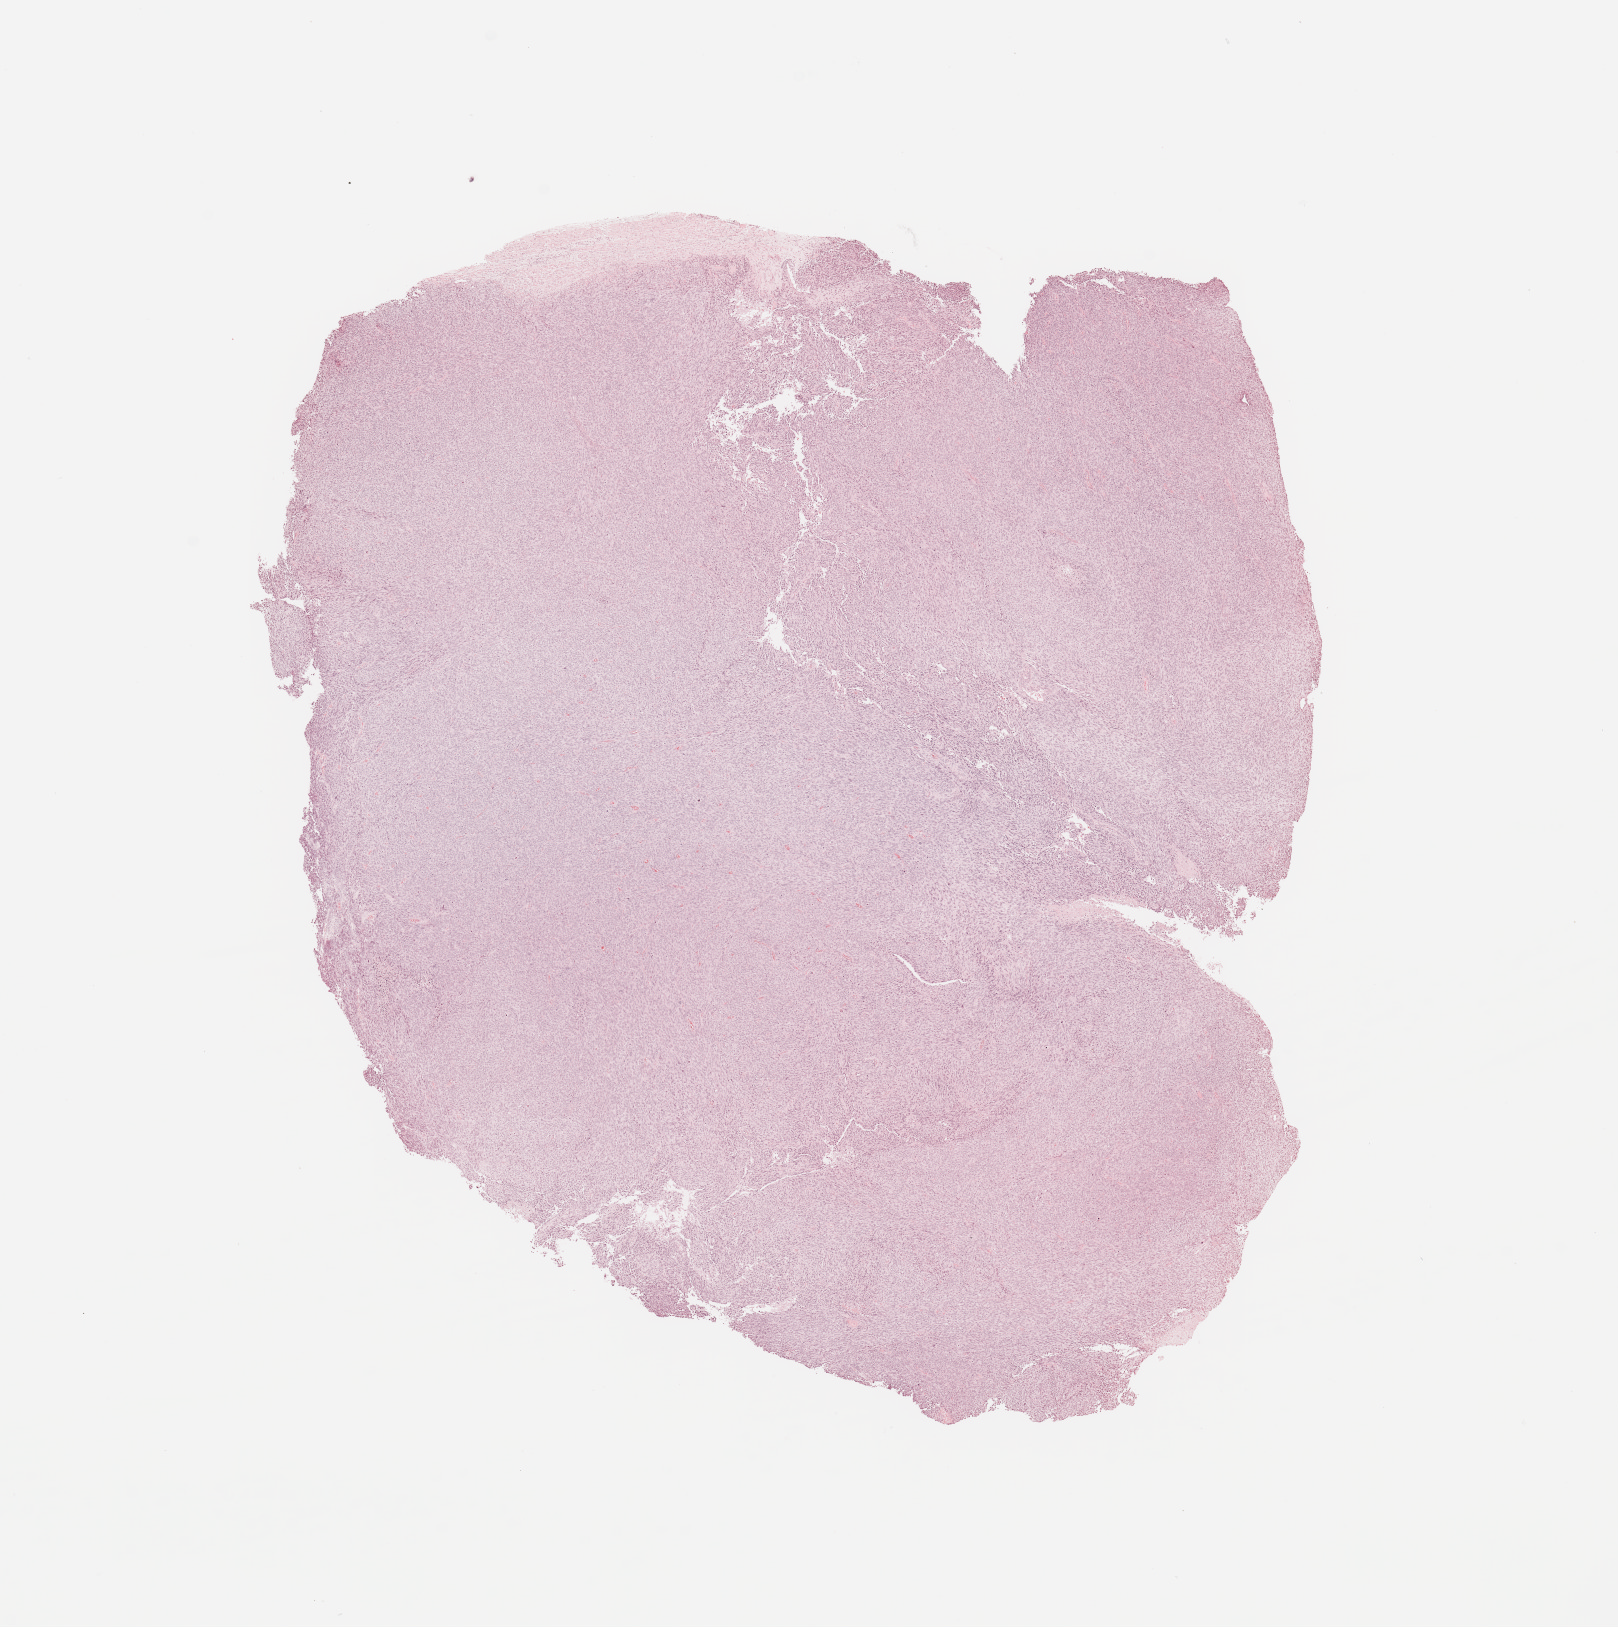
H&E-stained whole-slide image, shown as a low-resolution overview of the whole scanned area (about 12.8 x 12.9 mm, slide scanned at 20x); tumour tissue sample. 23-year-old female patient.
Patient diagnosis (cohort enrolment): sarcoma (site not recorded at cohort level). Primary tumour site (as recorded): lower extremity.